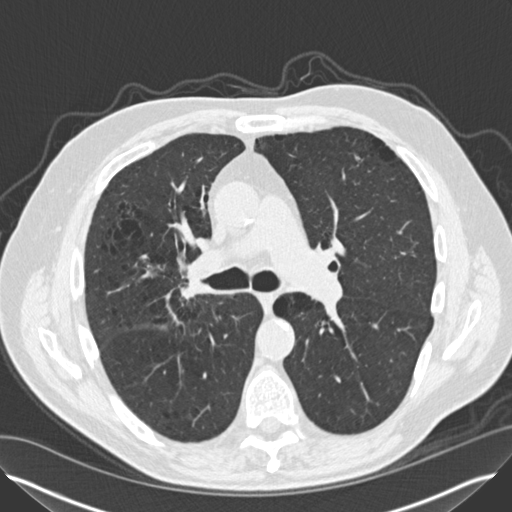
Low-dose screening chest CT, one axial slice. Position 87 of 149 along the scan axis. Reconstruction kernel B30f. 120 kVp. Lung window (W 1500 / L -600 HU). 2 mm slice thickness. 512 × 512 image matrix, field of view 370 × 370 mm.
Annotated regions visible in this slice (expert manual segmentation):
- lesion 2 (tumor, hilum of right lung): bounding box <188,270,208,297> (left, top, right, bottom; pixels)